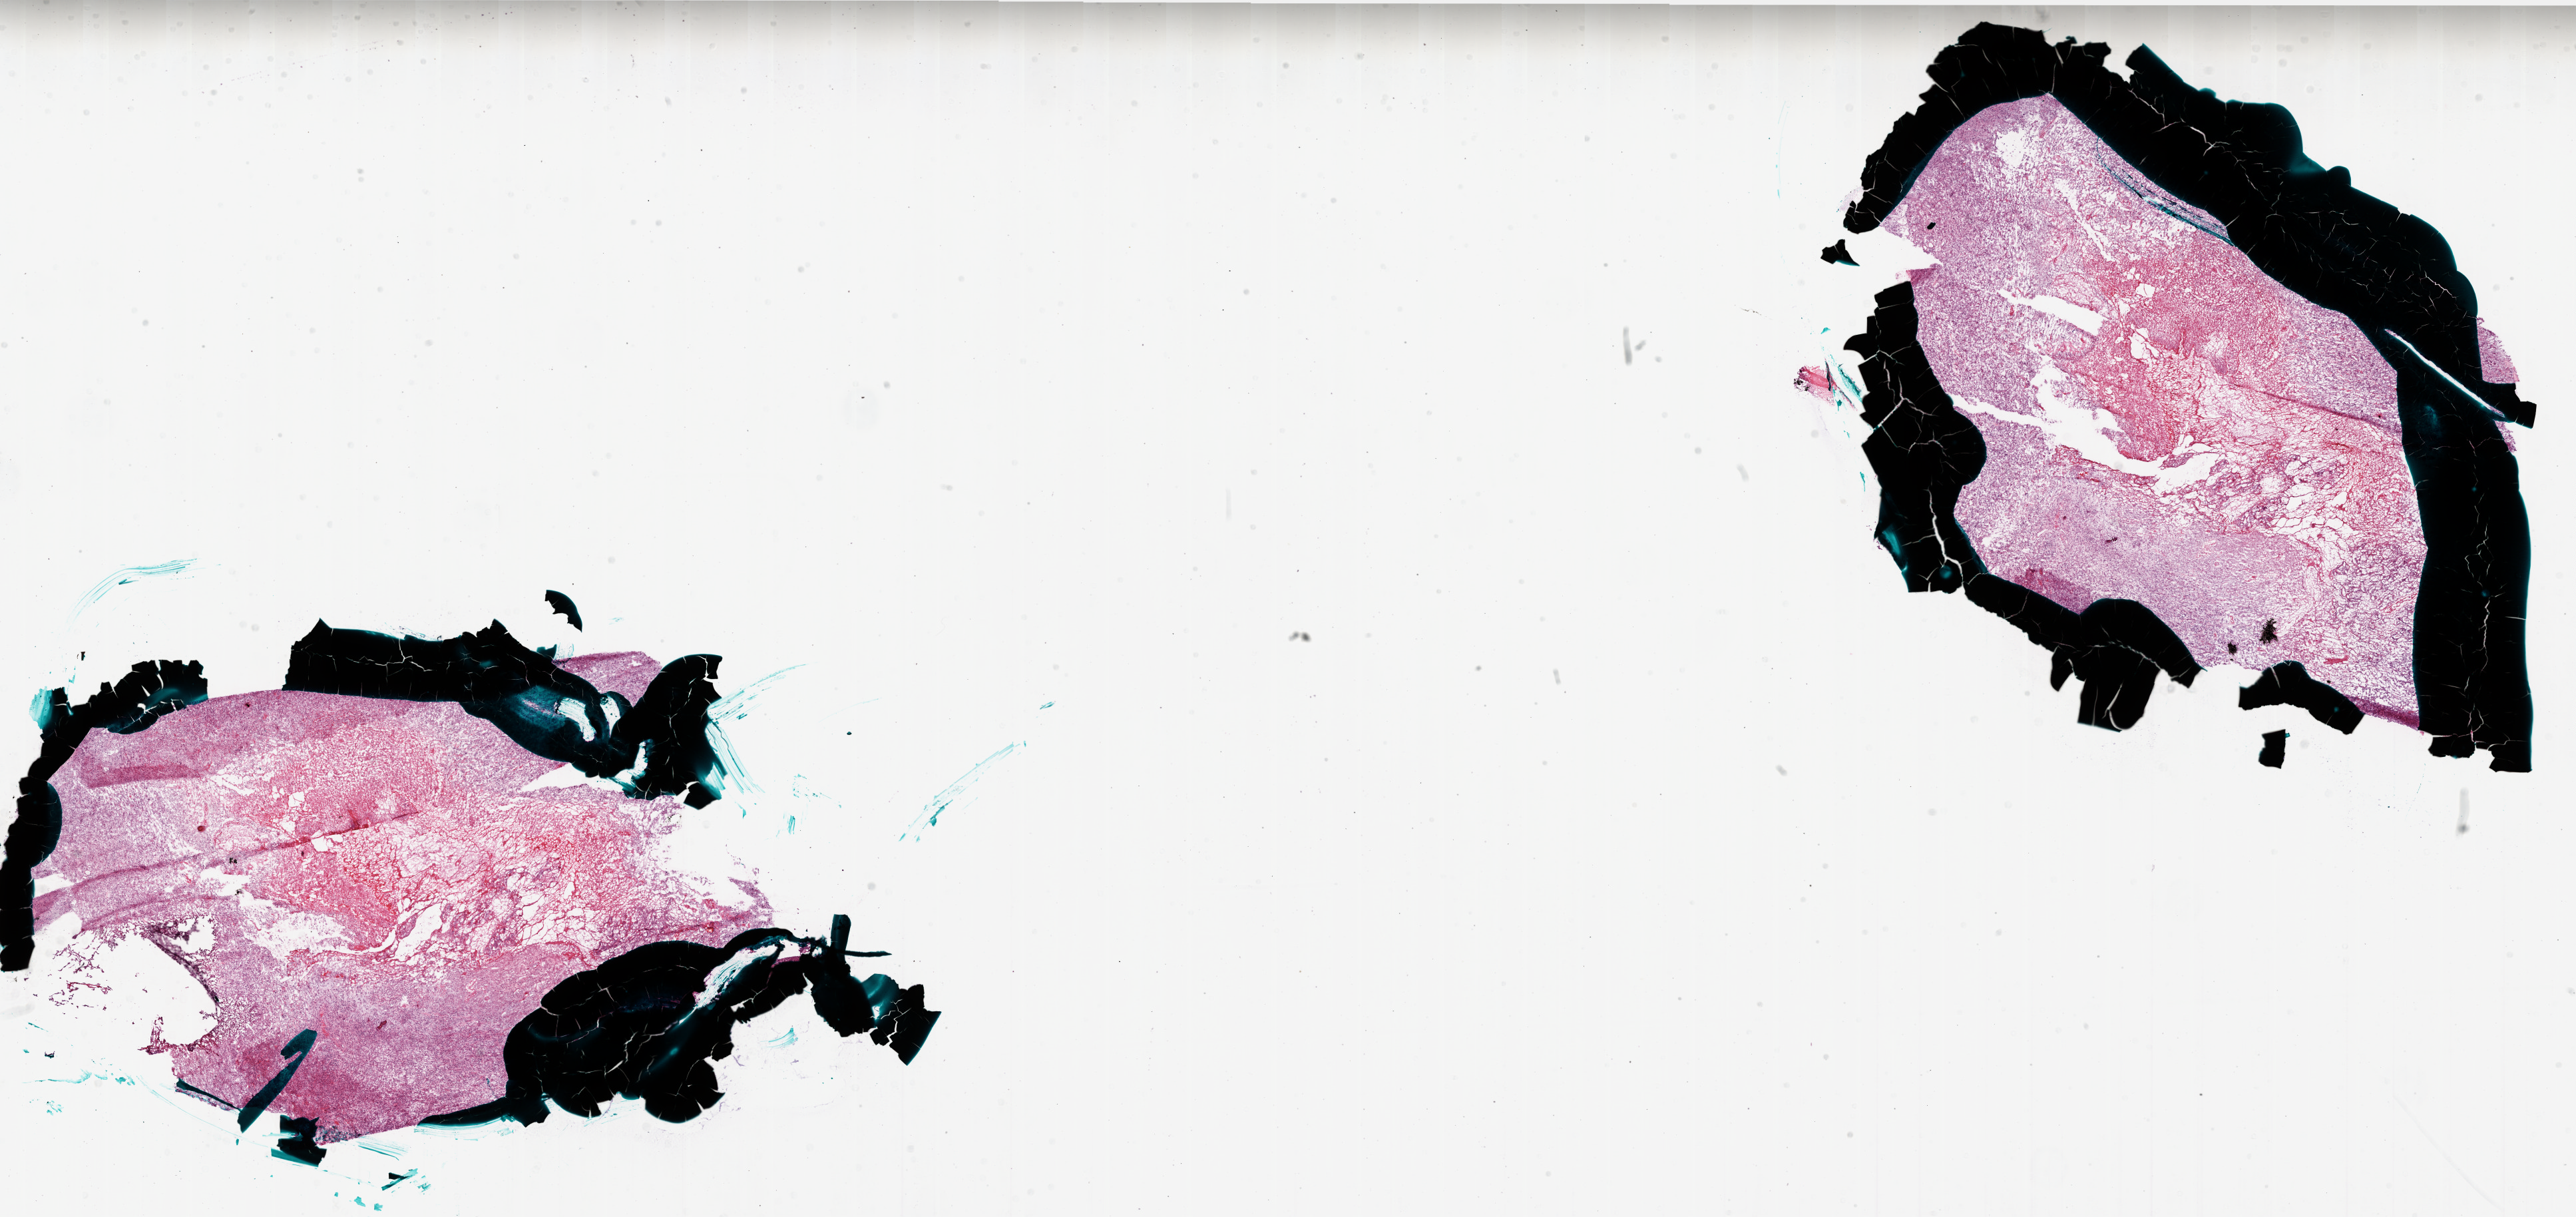
Digitized Hematoxylin and eosin (H&E) stained tissue section (whole slide) — whole scanned area (about 31.0 x 14.6 mm, slide scanned at 20x) shown as a low-resolution overview. Frozen section. Sample: primary tumour, brain. Female patient; age at initial diagnosis 51 years. Pathologist review of this section (percent, as recorded): tumour cells 60%, tumour nuclei 100%, normal cells 0%, stromal cells 0%, necrosis 40%. Inflammatory infiltration, as recorded: lymphocyte infiltration 0%, monocyte infiltration 0%, neutrophil infiltration 0%.
Pathologic diagnosis: Glioblastoma.